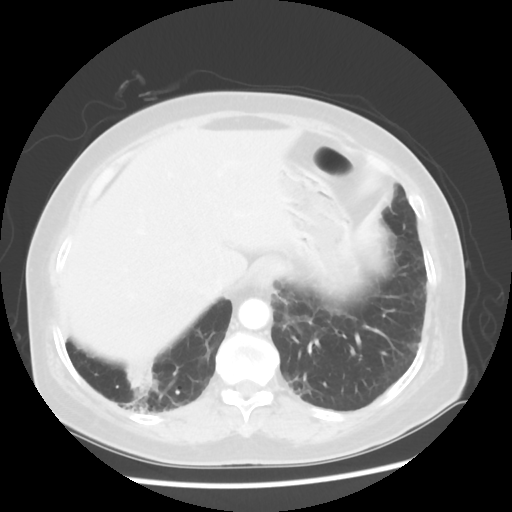
Chest CT, one axial slice. Slice 12 of 56 in the series (ordered by position). Reconstruction kernel STANDARD. 120 kVp. Lung window (W 1500 / L -600 HU). 512 × 512 image matrix, field of view 360 × 360 mm. Patient: female, 64 years. From the clinical record (not read from this slice): clinical TNM (as recorded): Tis N0 M0.
Outlined on this slice (bounding box drawn by a radiologist):
- lung tumour (recorded histology: adenocarcinoma): bounding box (x1, y1, x2, y2) in pixels: (111, 353, 172, 433)